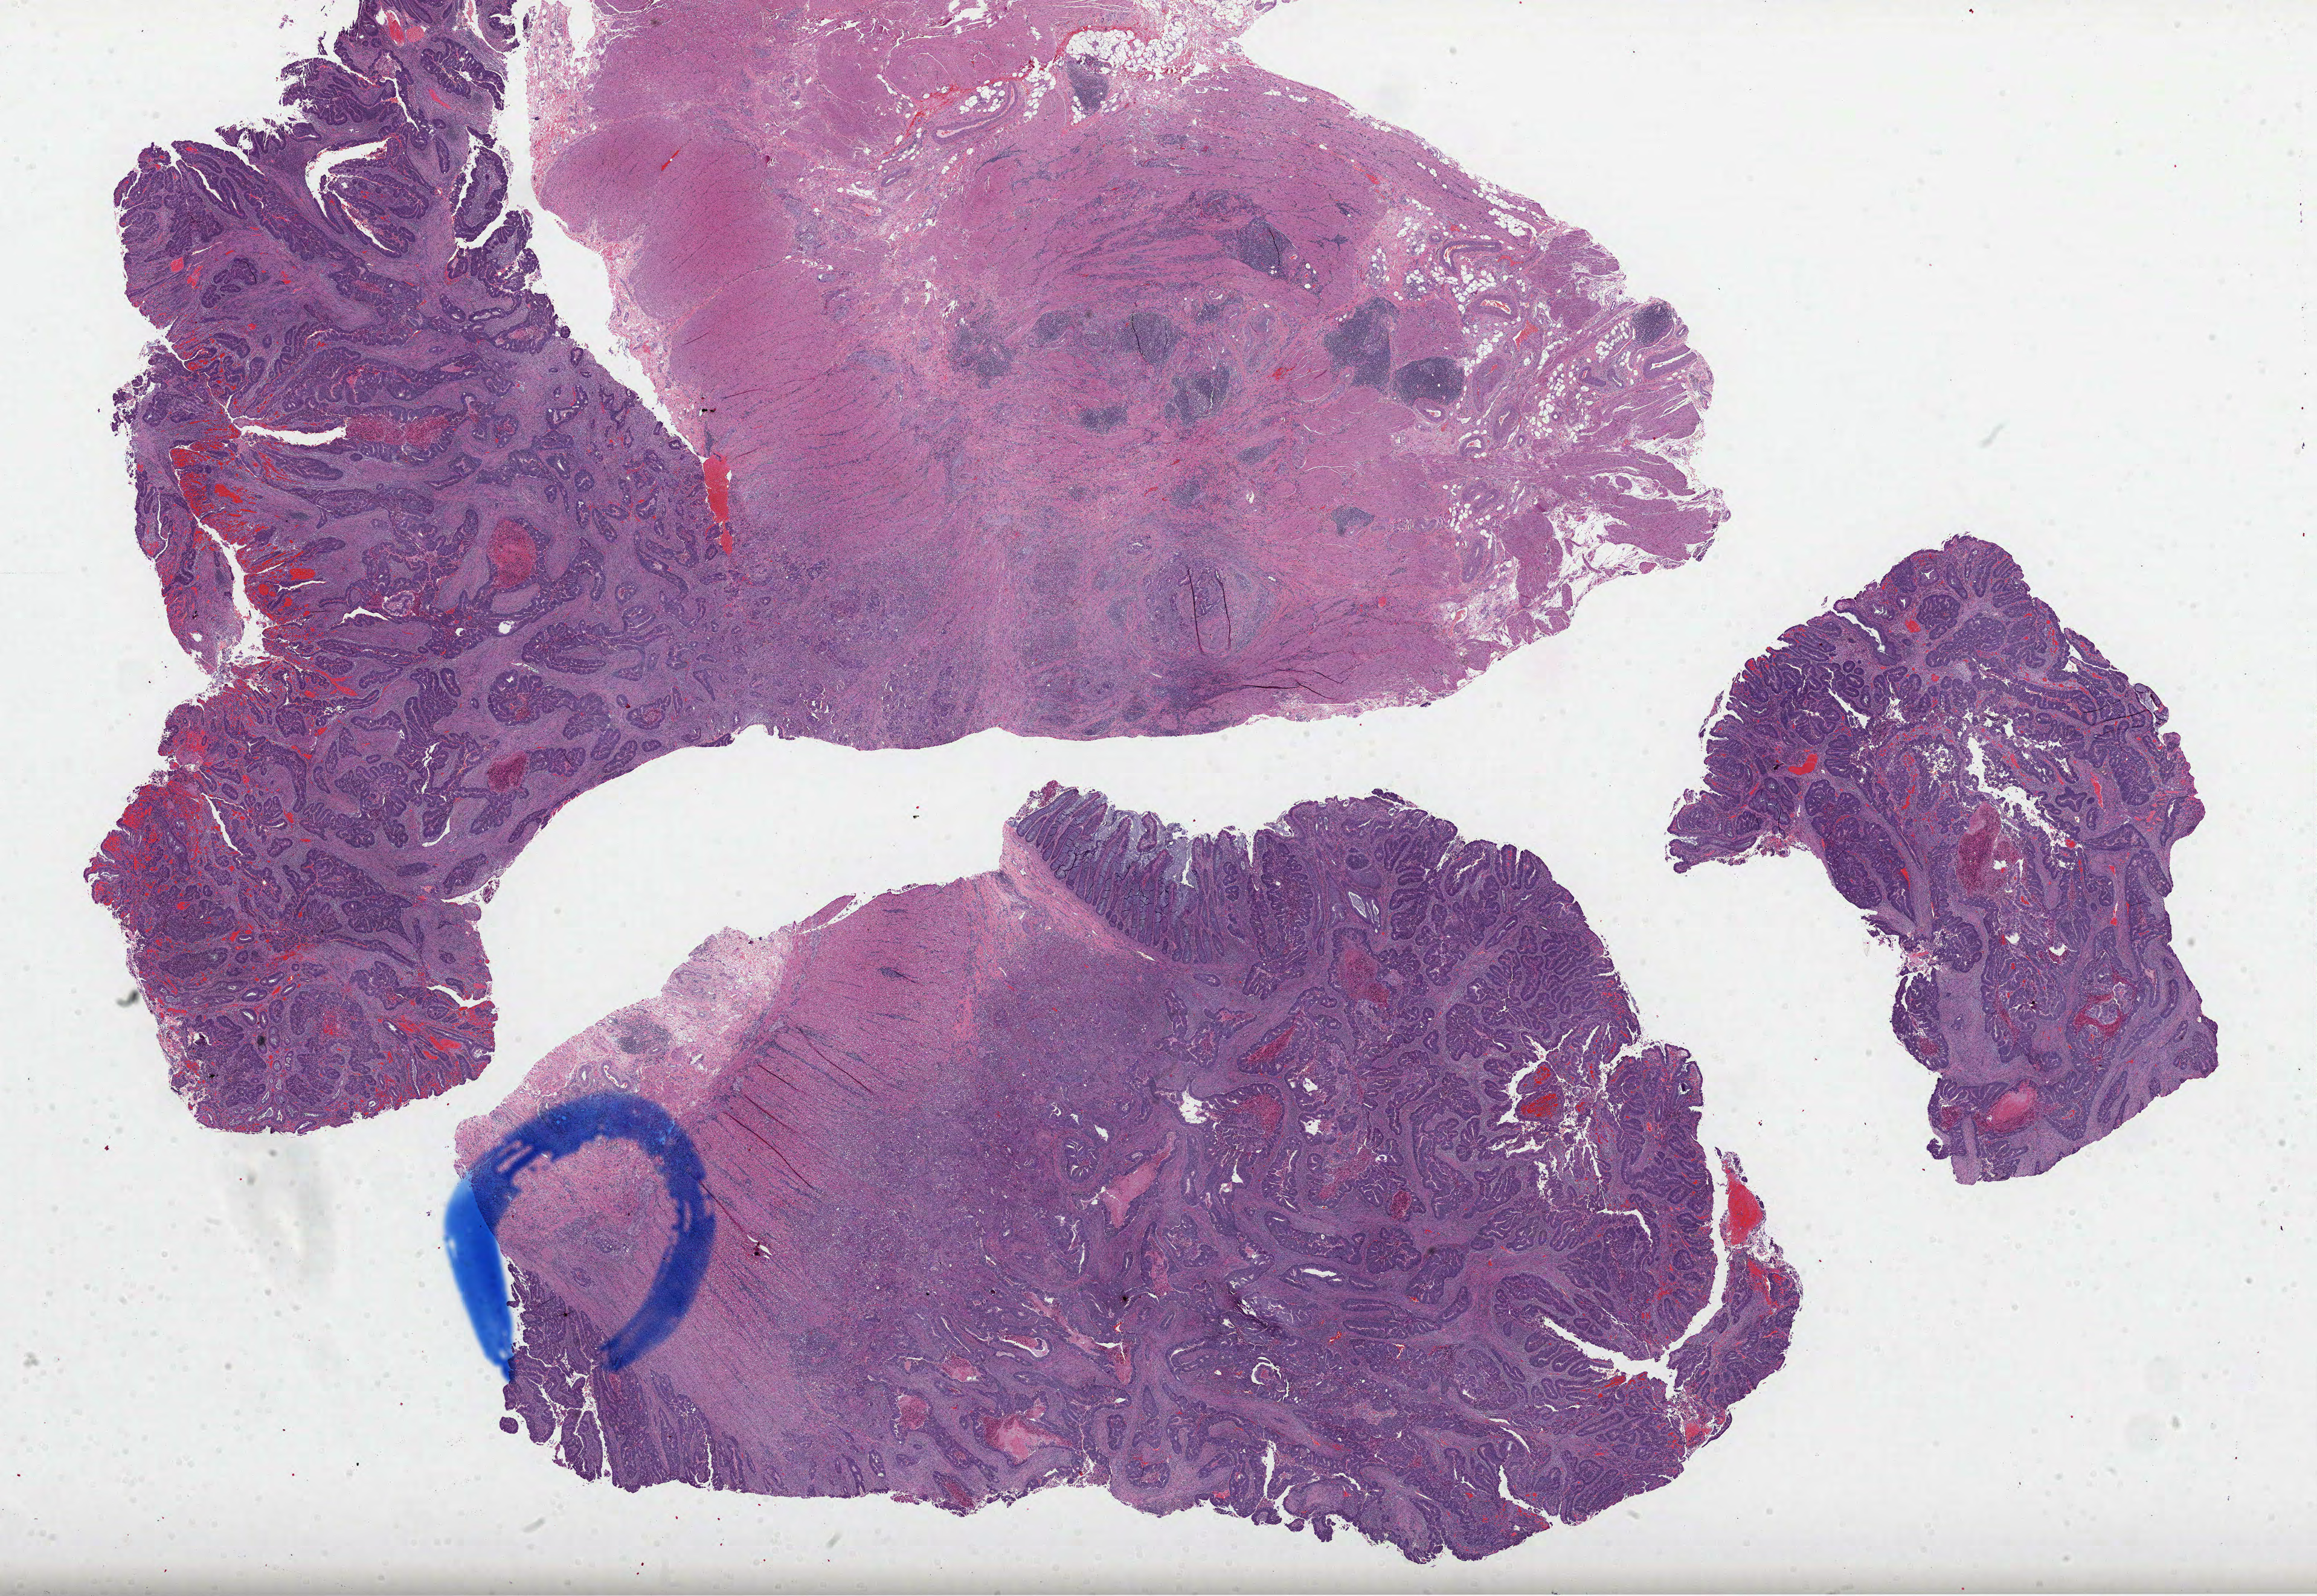
Digitized Hematoxylin and eosin (H&E) stained tissue section (whole slide), shown as a low-resolution overview of the whole scanned area (about 30.9 x 21.3 mm, from a 40x scan), formalin-fixed paraffin-embedded (FFPE) diagnostic section, sample: primary tumour, rectum. Patient: female, age at initial diagnosis 62 years.
Lymph nodes positive (case pathology): 1 of 19 examined. AJCC pathologic stage: IIIB (7th edition). Diagnosis: Adenocarcinoma, NOS.